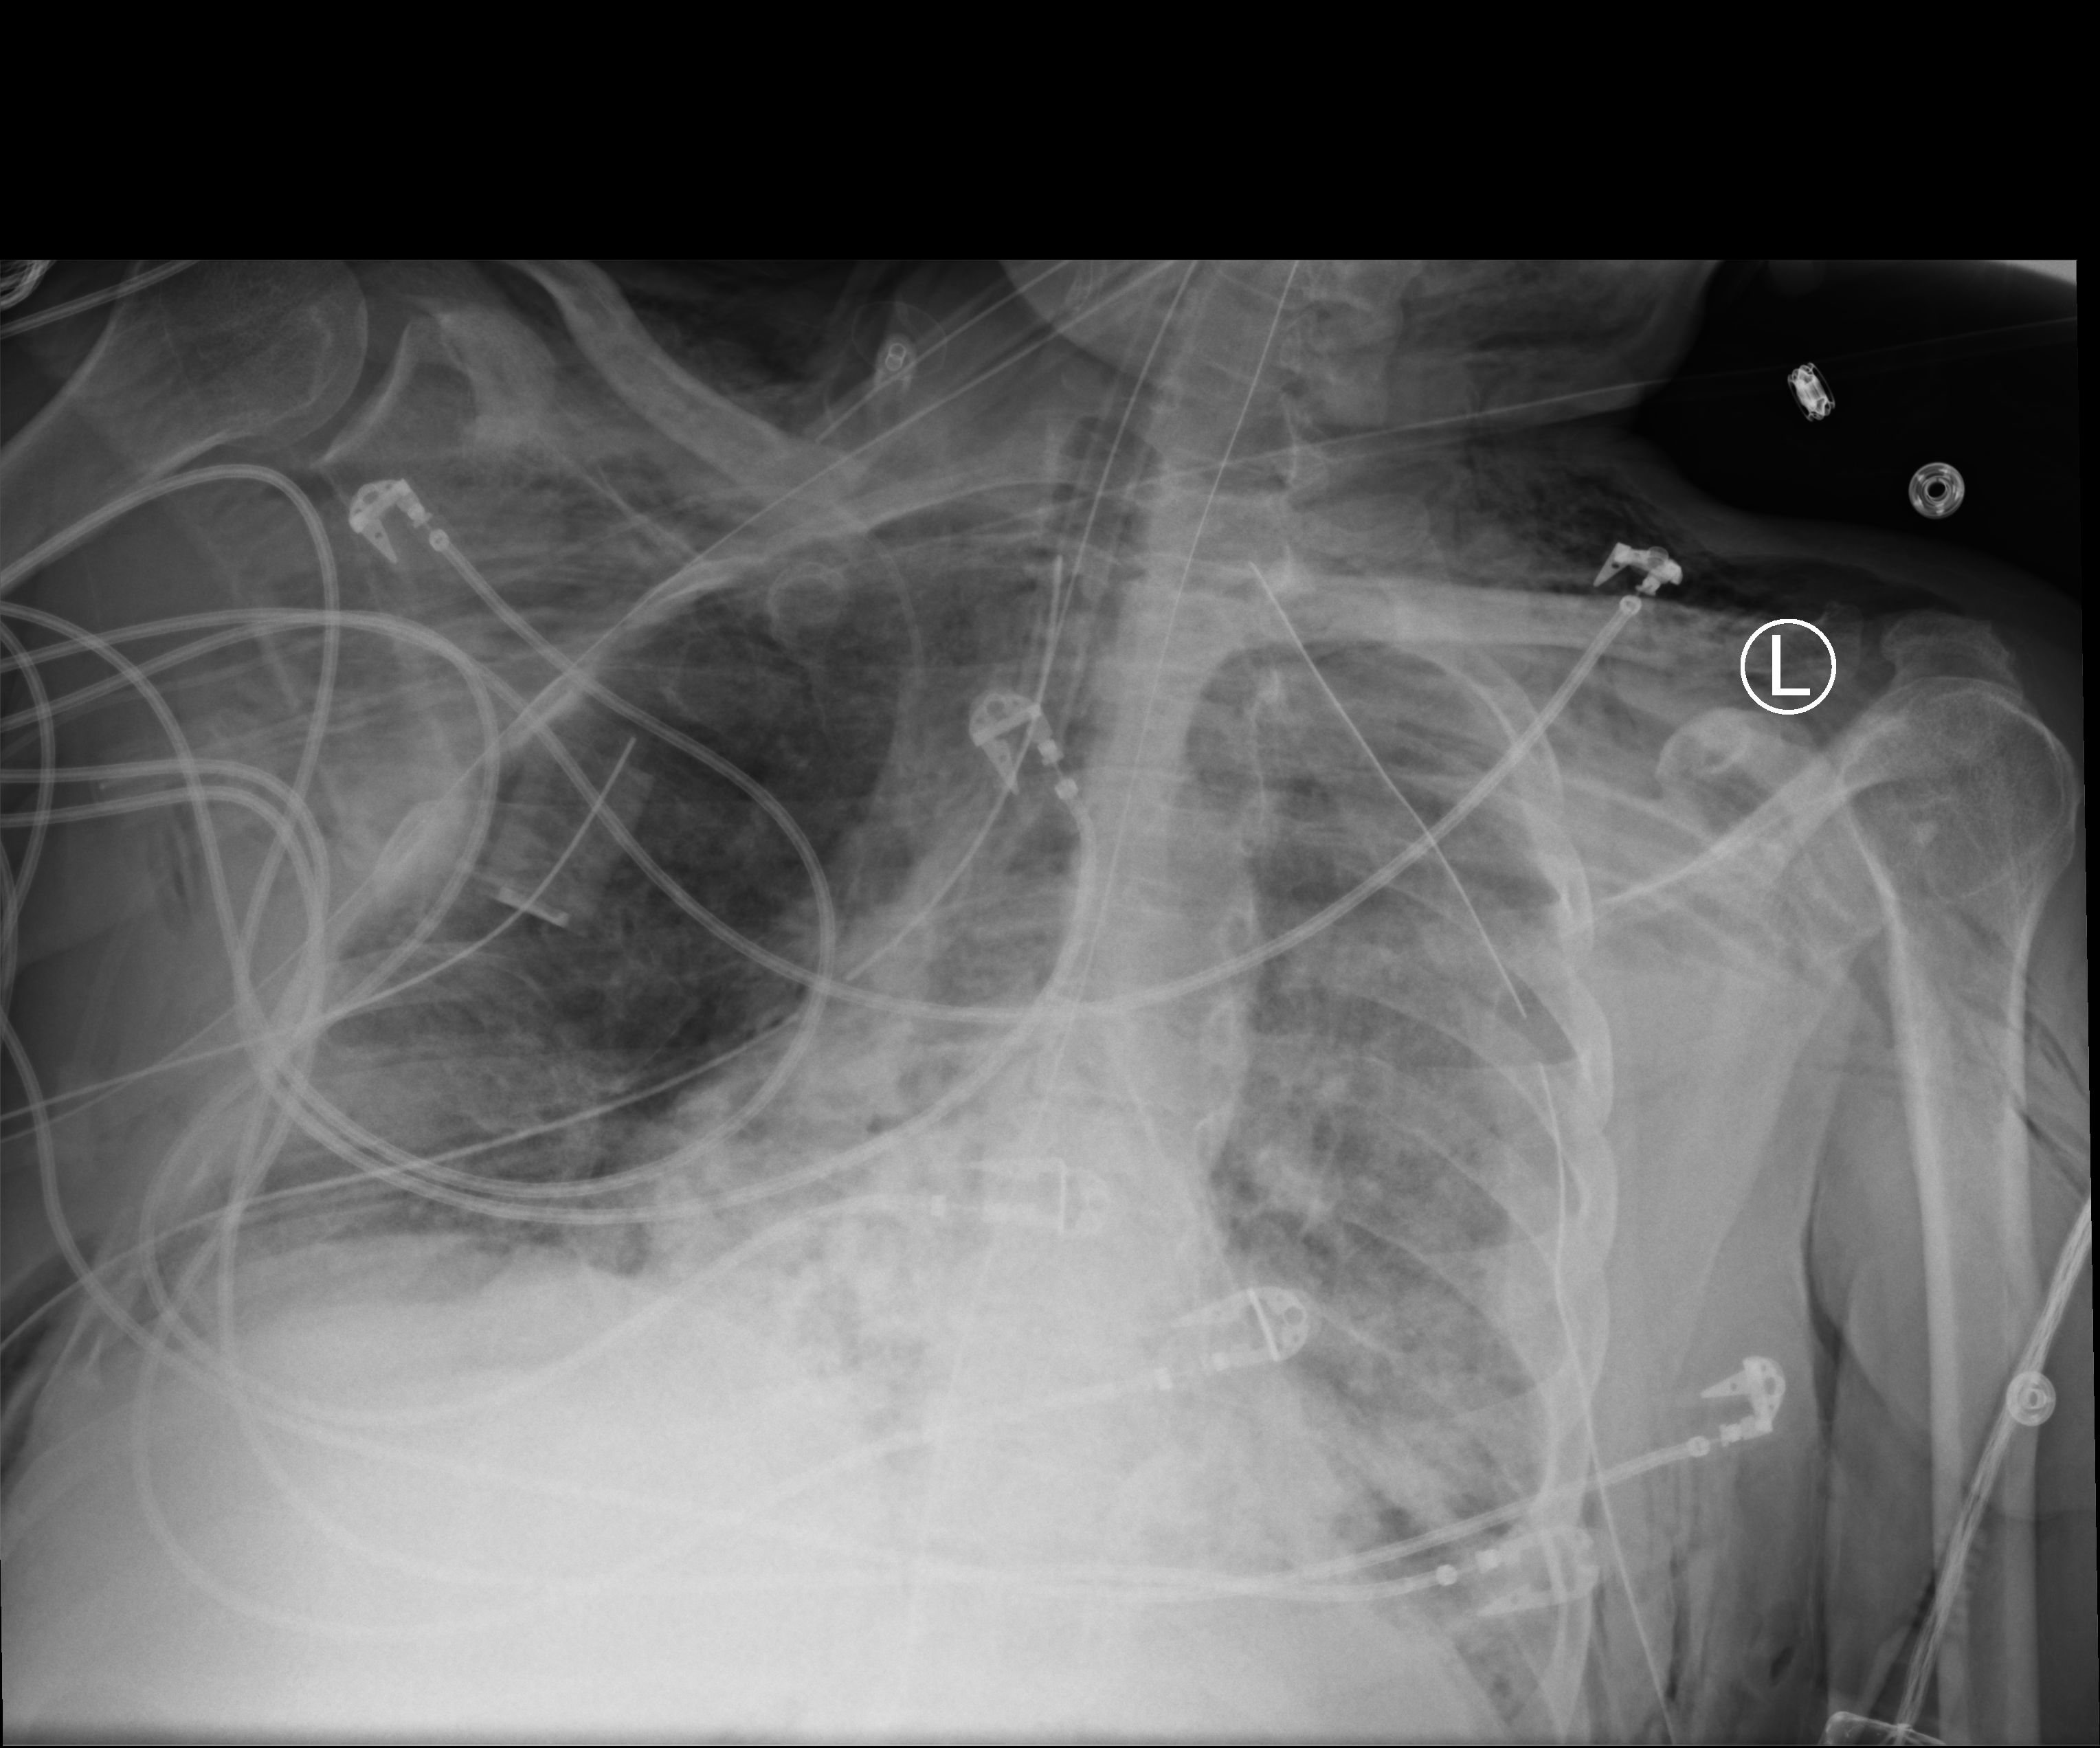
Bedside chest radiograph (computed radiography). Male patient hospitalised with COVID-19, age 18–59 years.
Hospital-stay facts (about this admission, not read from this image; timing relative to this image not recorded): admitted to intensive care during this hospital stay: yes; mechanically ventilated during this hospital stay: yes.